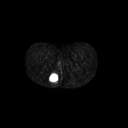
FDG PET of an extremity soft-tissue mass (from a PET/CT study), one axial slice; position 21 of 267 along the scan axis; 3.27 mm slice thickness; 128 × 128 image matrix, field of view 700 × 700 mm. Female patient, age 17 years. Case-level facts recorded for this patient, not image findings: histological type: epithelioid sarcoma; grade: intermediate; site of the primary tumour: right buttock.
Annotated regions visible in this slice (expert contour drawn on MRI and transferred to this co-registered scan by the dataset authors):
- gross tumour volume including surrounding oedema: box from (x=48, y=73) to (x=60, y=86) px
- gross tumour volume (mass): (x=49, y=74)–(x=58, y=82)